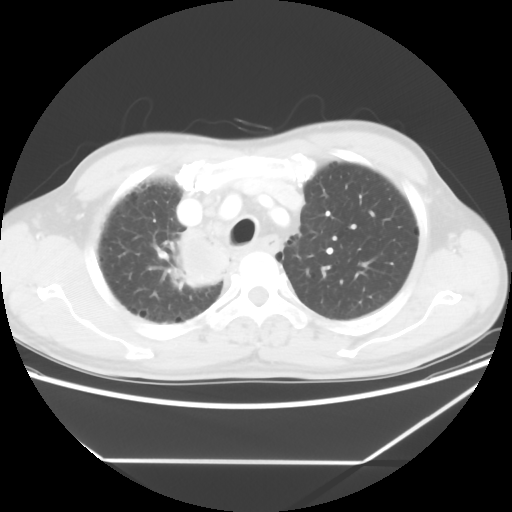
Chest CT, one axial slice. Slice 48 of 60 in the series (ordered by position). Reconstruction kernel STANDARD. Lung window (W 1500 / L -600 HU). 5 mm slice thickness. 512 × 512 image matrix. Male patient, age 58 years. From the clinical record (not read from this slice): clinical TNM (as recorded): T2 N2 M0.
Outlined on this slice (rectangle marked by the reading radiologist):
- lung tumour (recorded histology: squamous cell carcinoma): bounding box (x1, y1, x2, y2) in pixels: (167, 227, 230, 295)